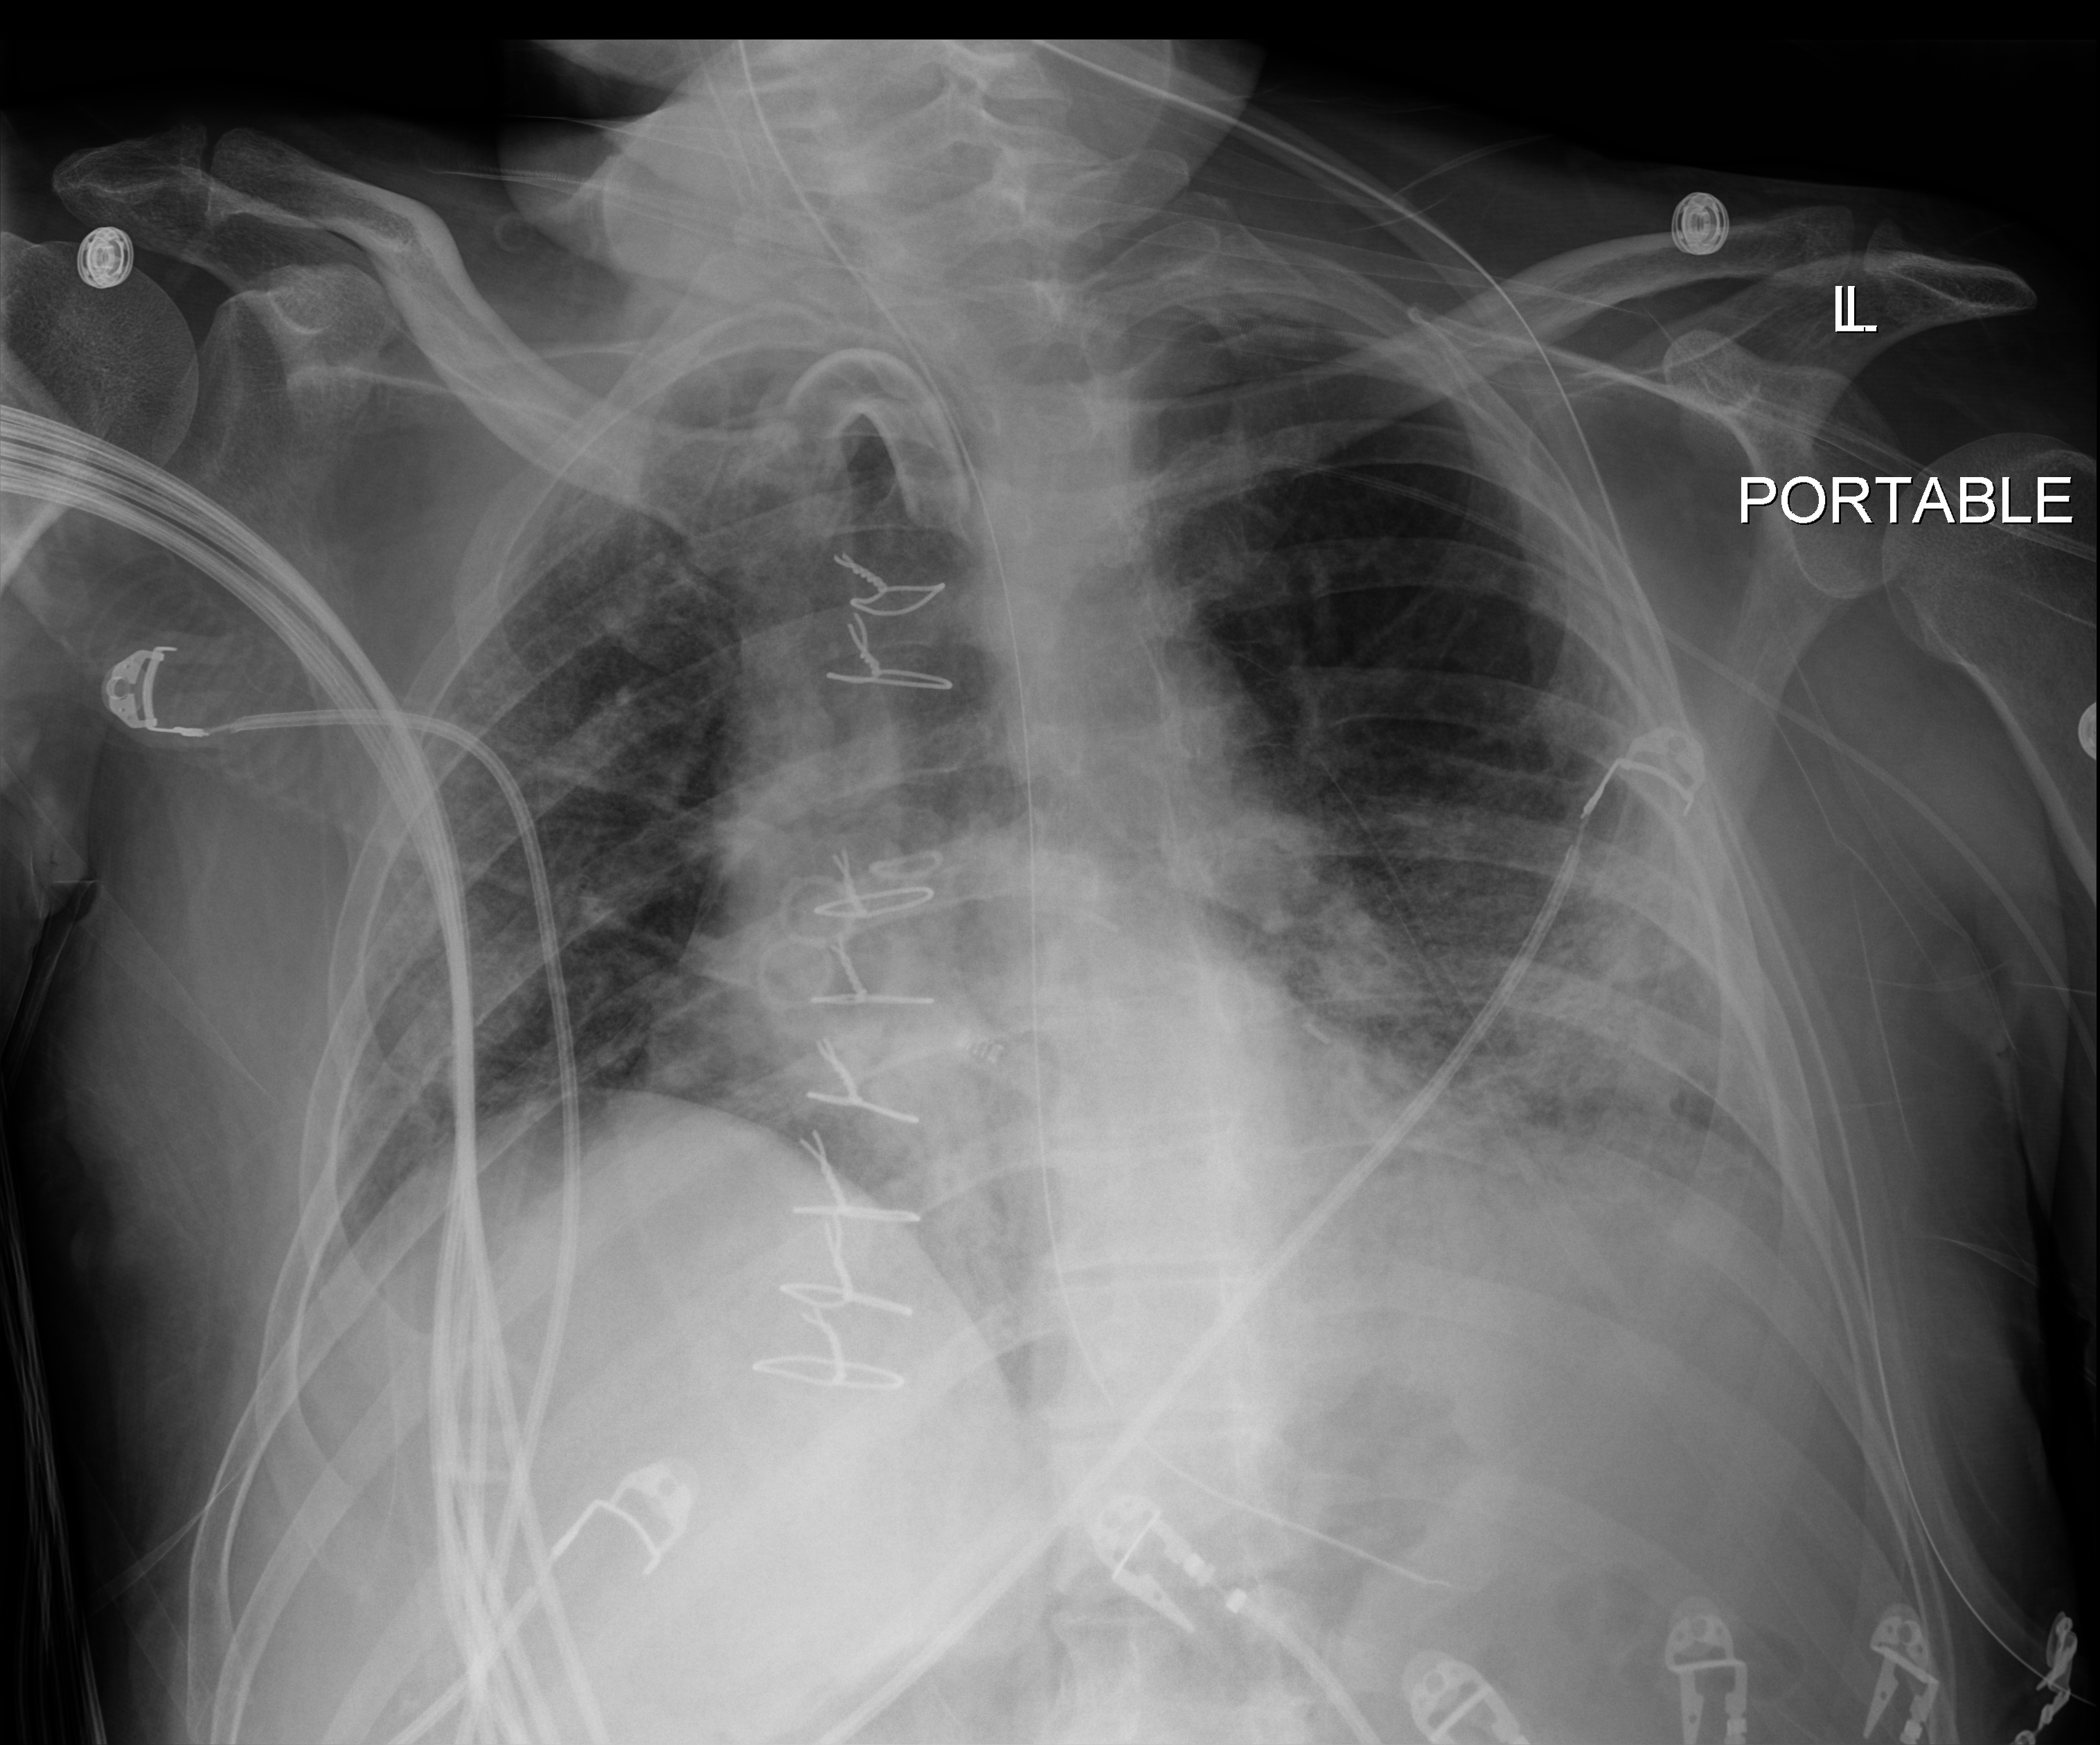
Portable chest radiograph, anteroposterior (AP) projection. Patient hospitalised with COVID-19; male, aged 18–59 years.
From the hospital-stay record, not from the radiograph (when in the stay this image was taken is not recorded):
- hypertension (admission record): no